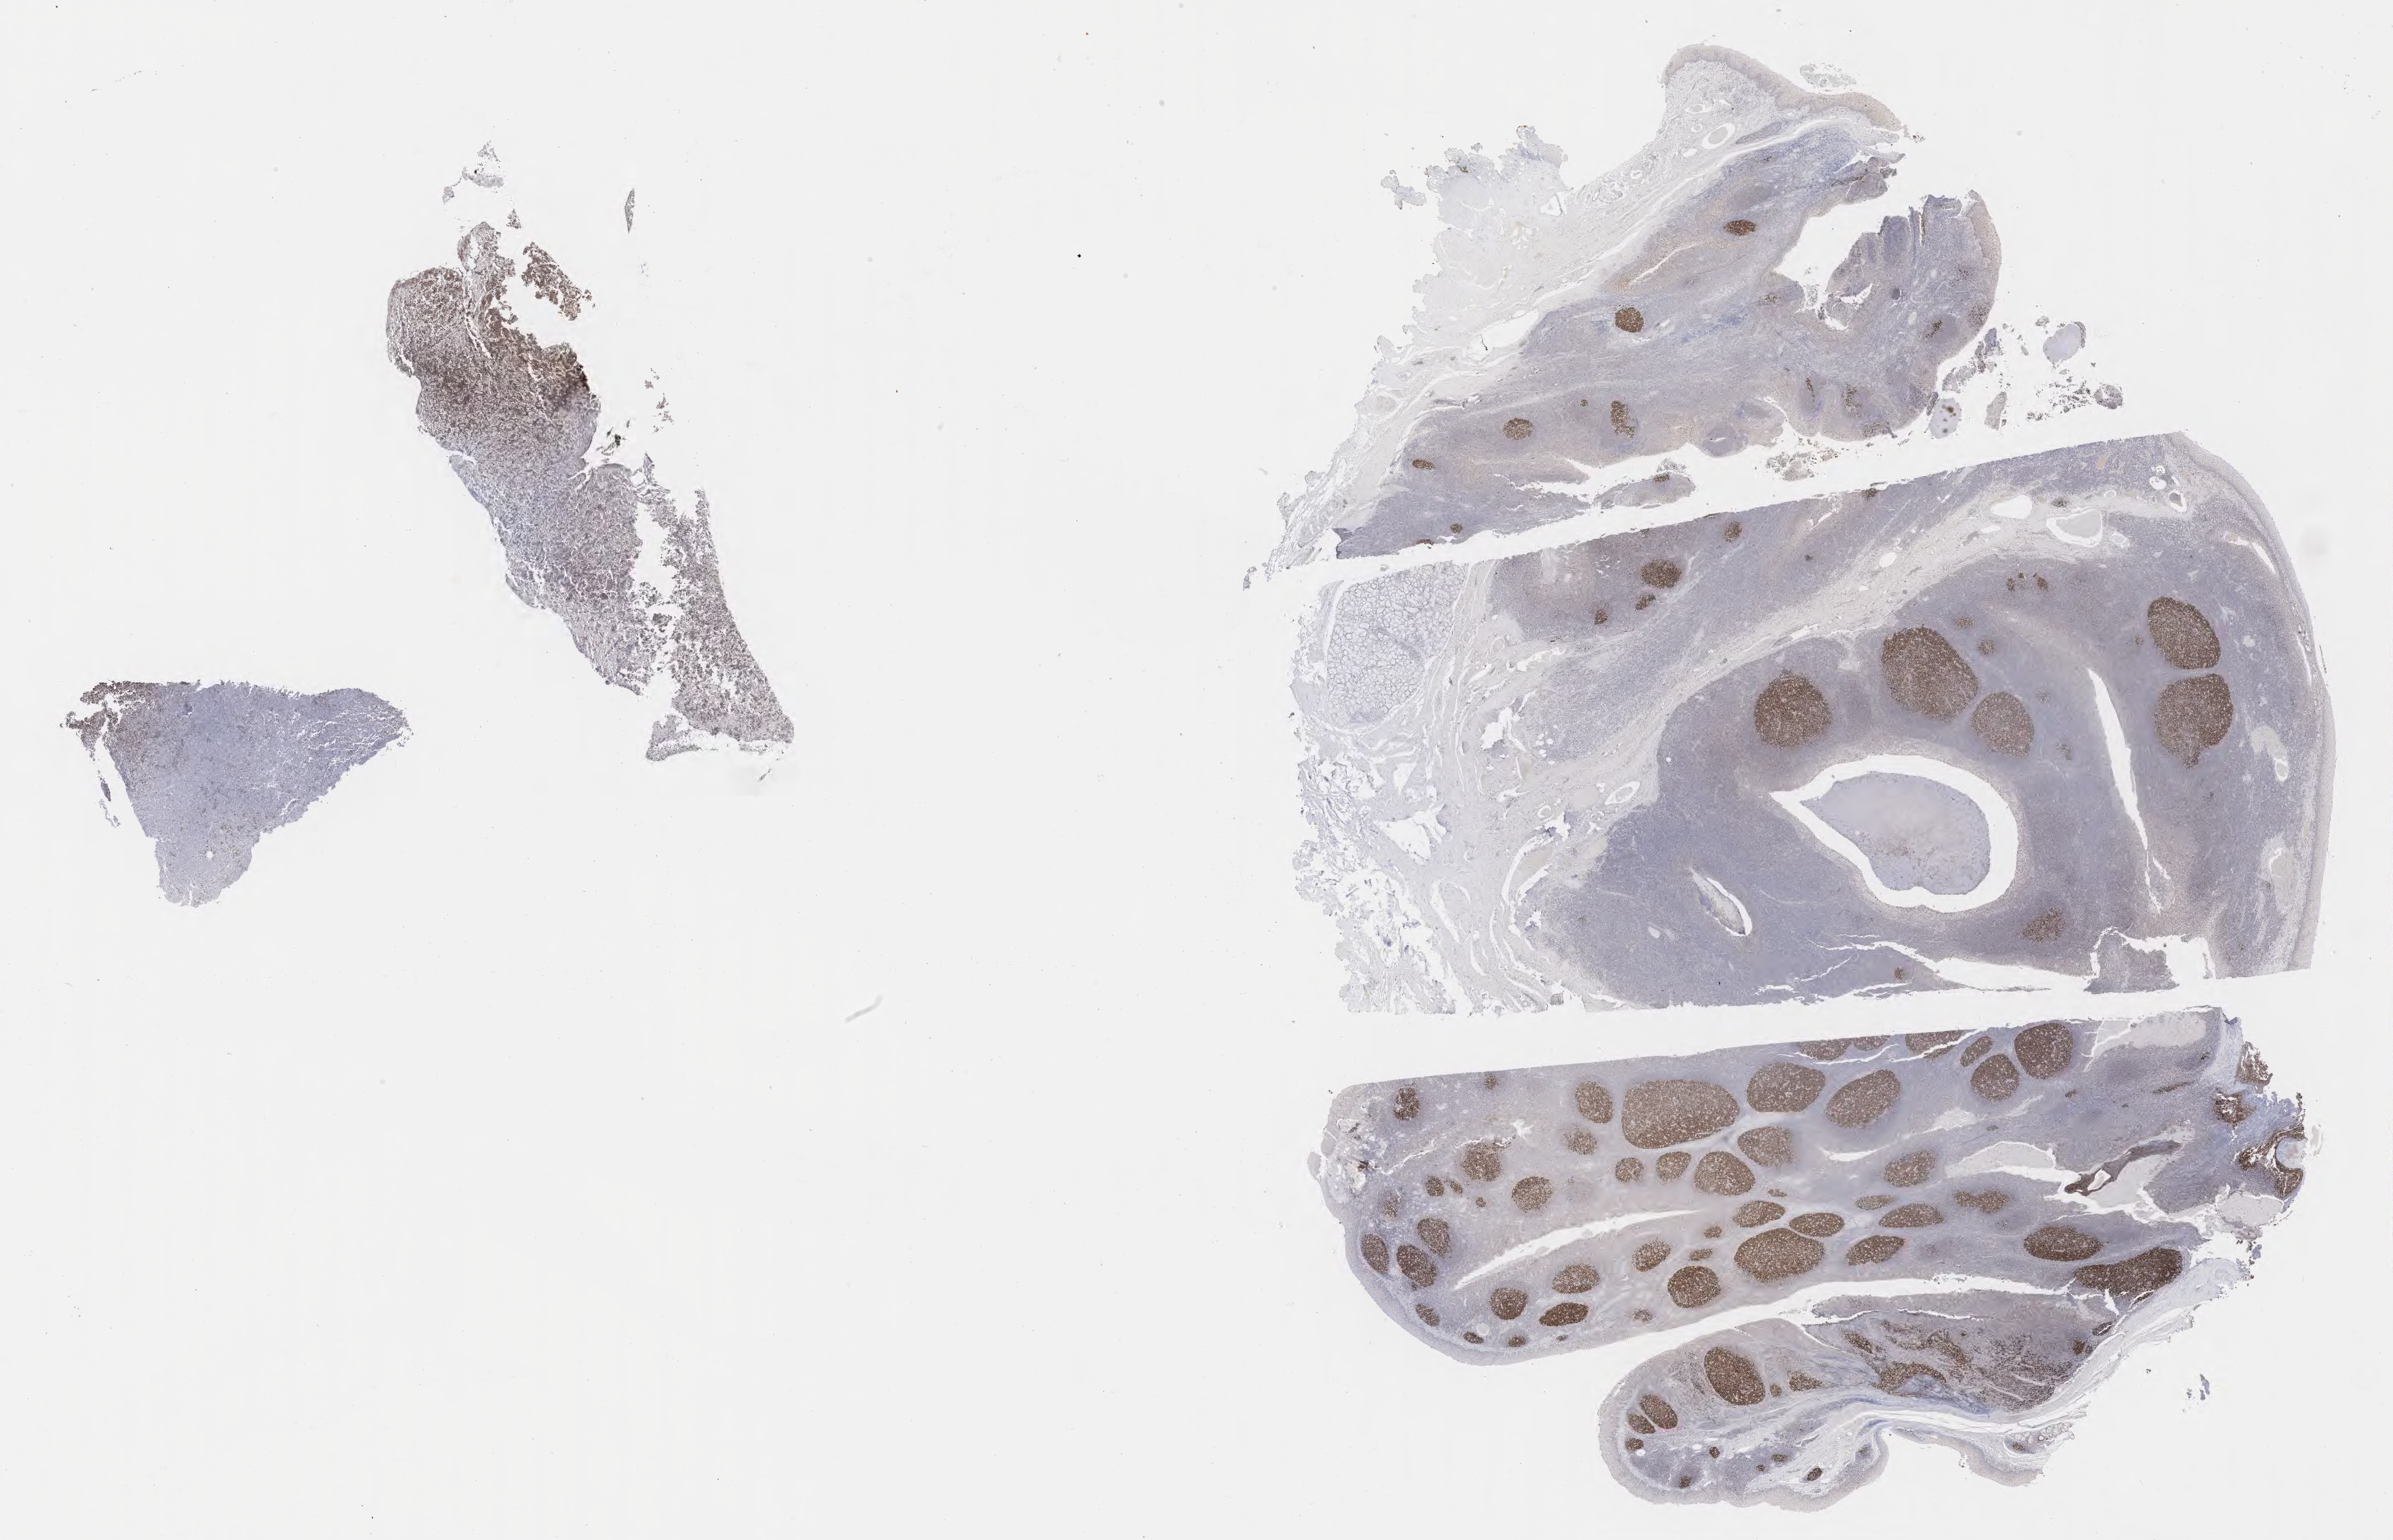
Whole-slide image, immunohistochemical stain for BCL6, a low-resolution overview of the entire scanned area, about 29.2 x 18.8 mm. Tumor tissue. Male patient; age at initial diagnosis 2 years.
Diagnosis: Burkitt lymphoma, NOS.